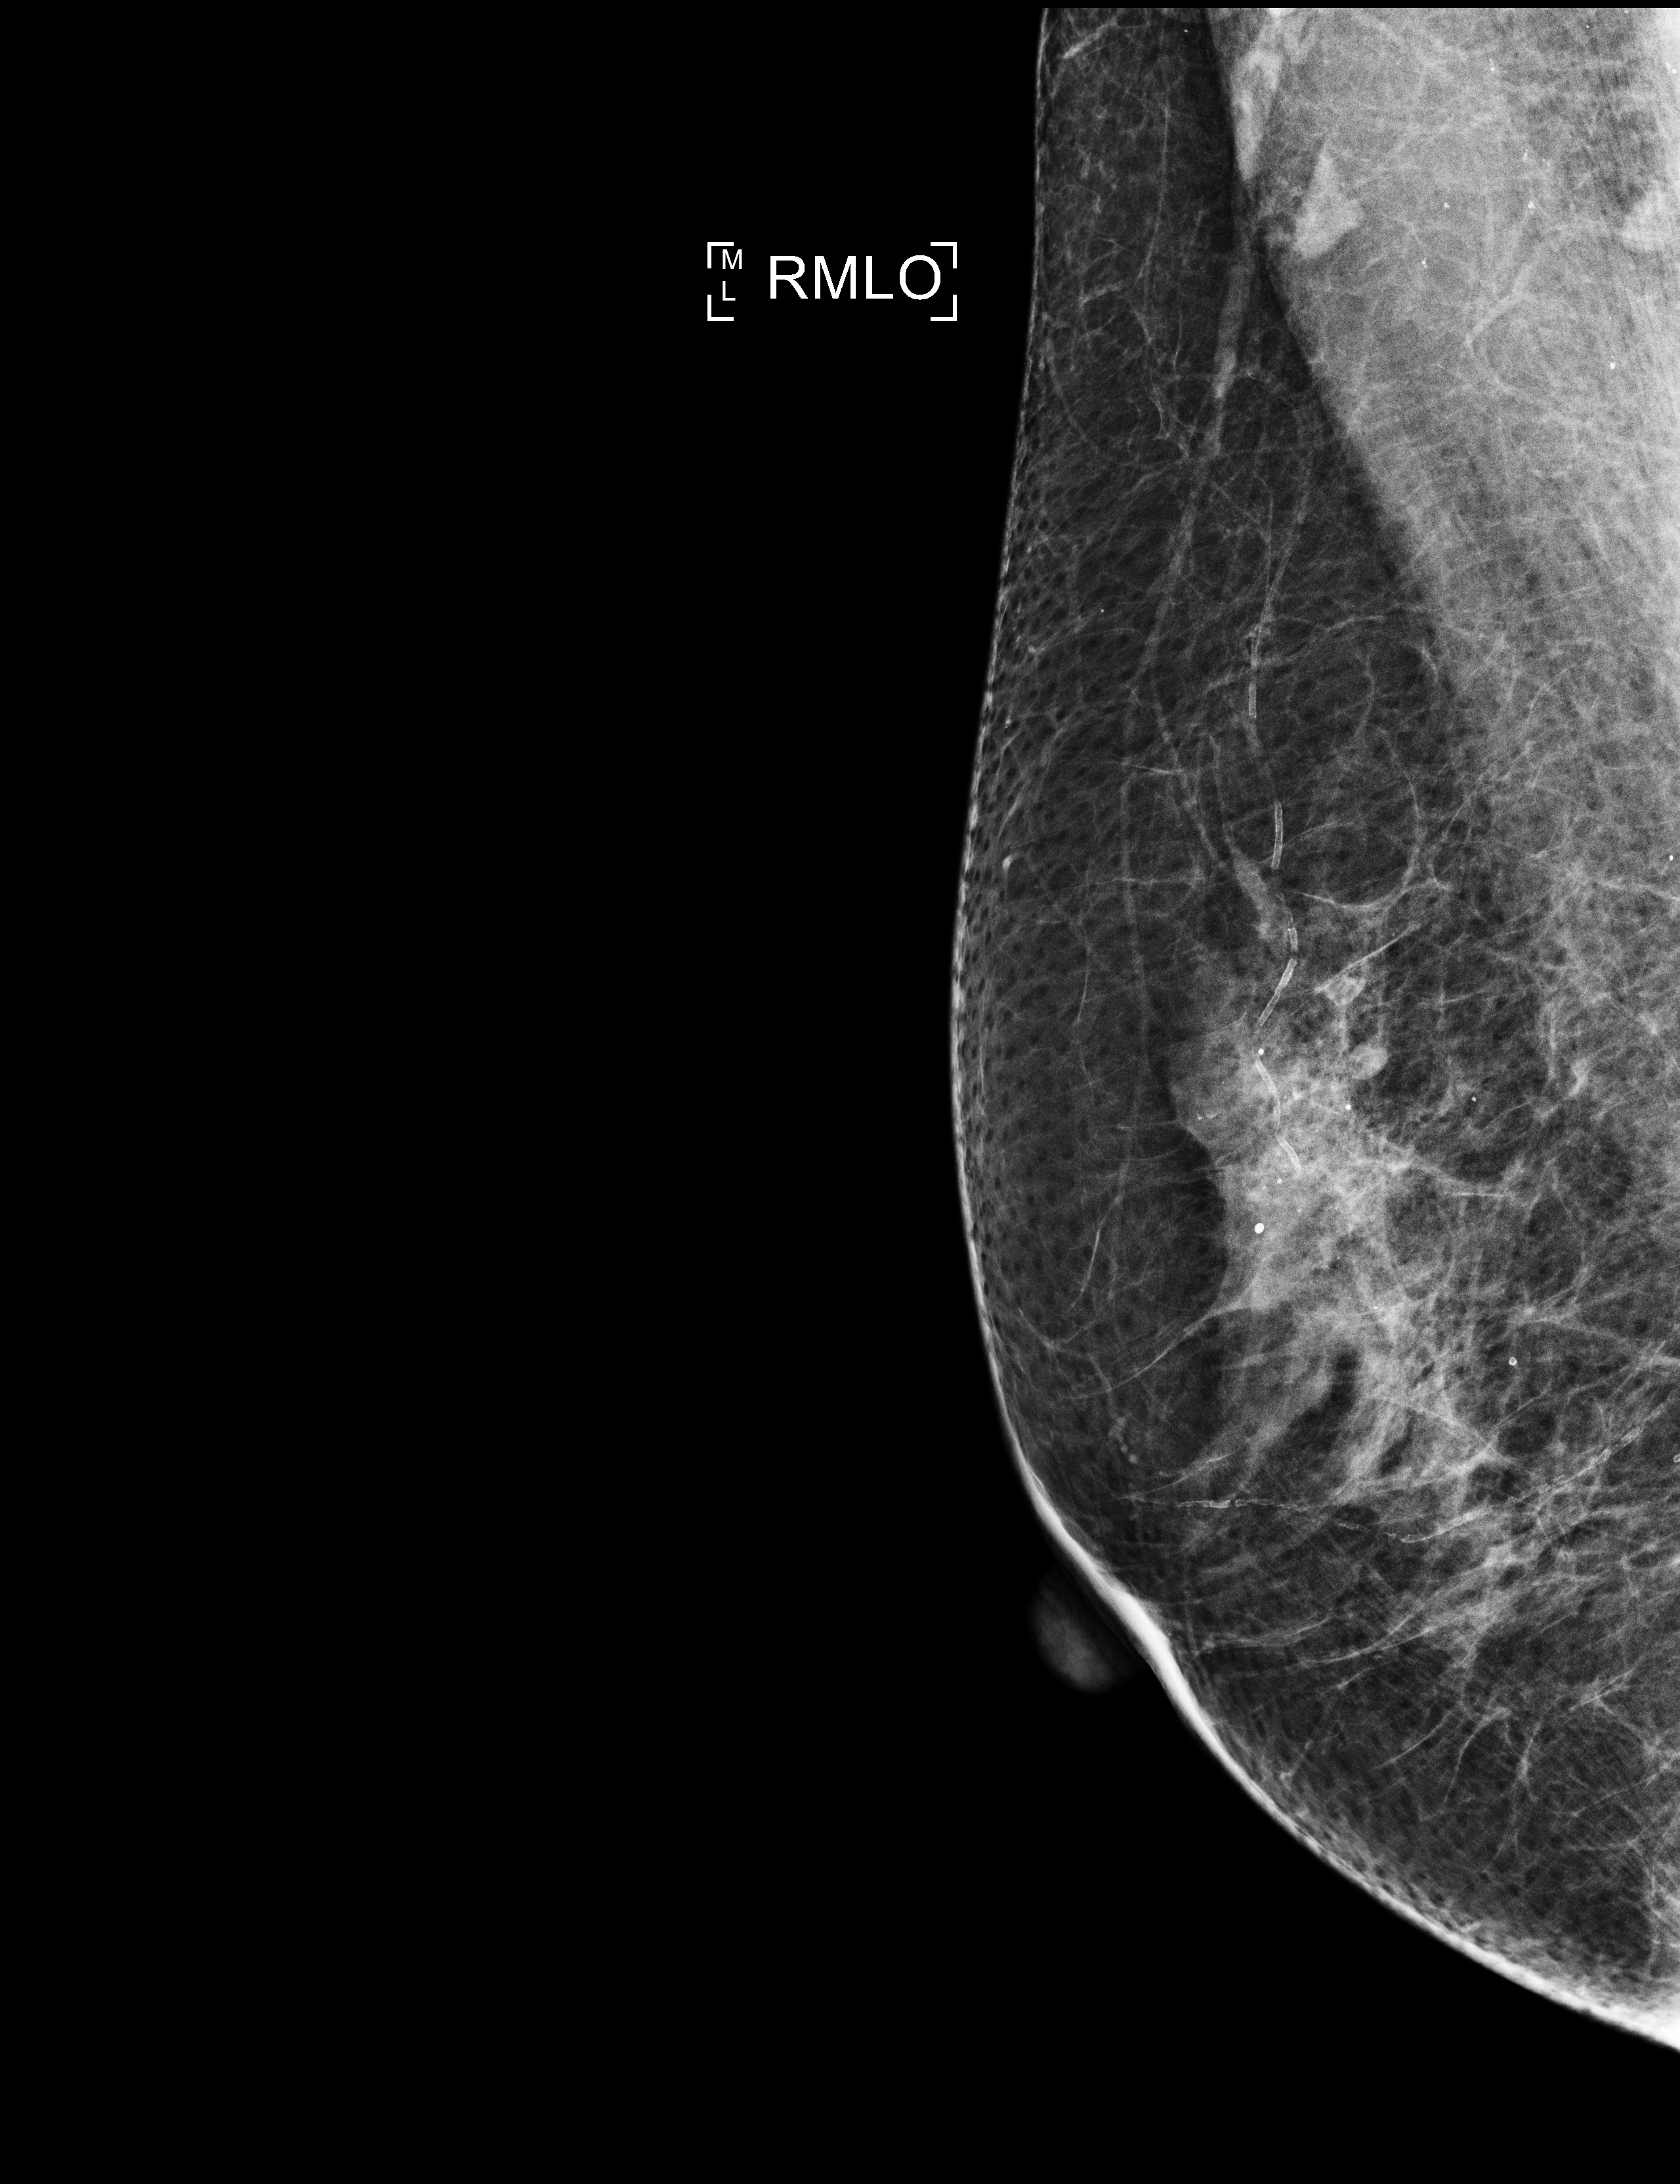
Digital mammogram (FFDM); right breast; mediolateral oblique (MLO) view; annual screening mammography examination; compressed breast thickness 59 mm. Patient aged 68 years (female).
Breast density at the screening exam (both breasts): heterogeneously dense (BI-RADS density category c). Final BI-RADS category for the screening round (tomosynthesis exam, both breasts): category 2. Recall: no recall after this screen.